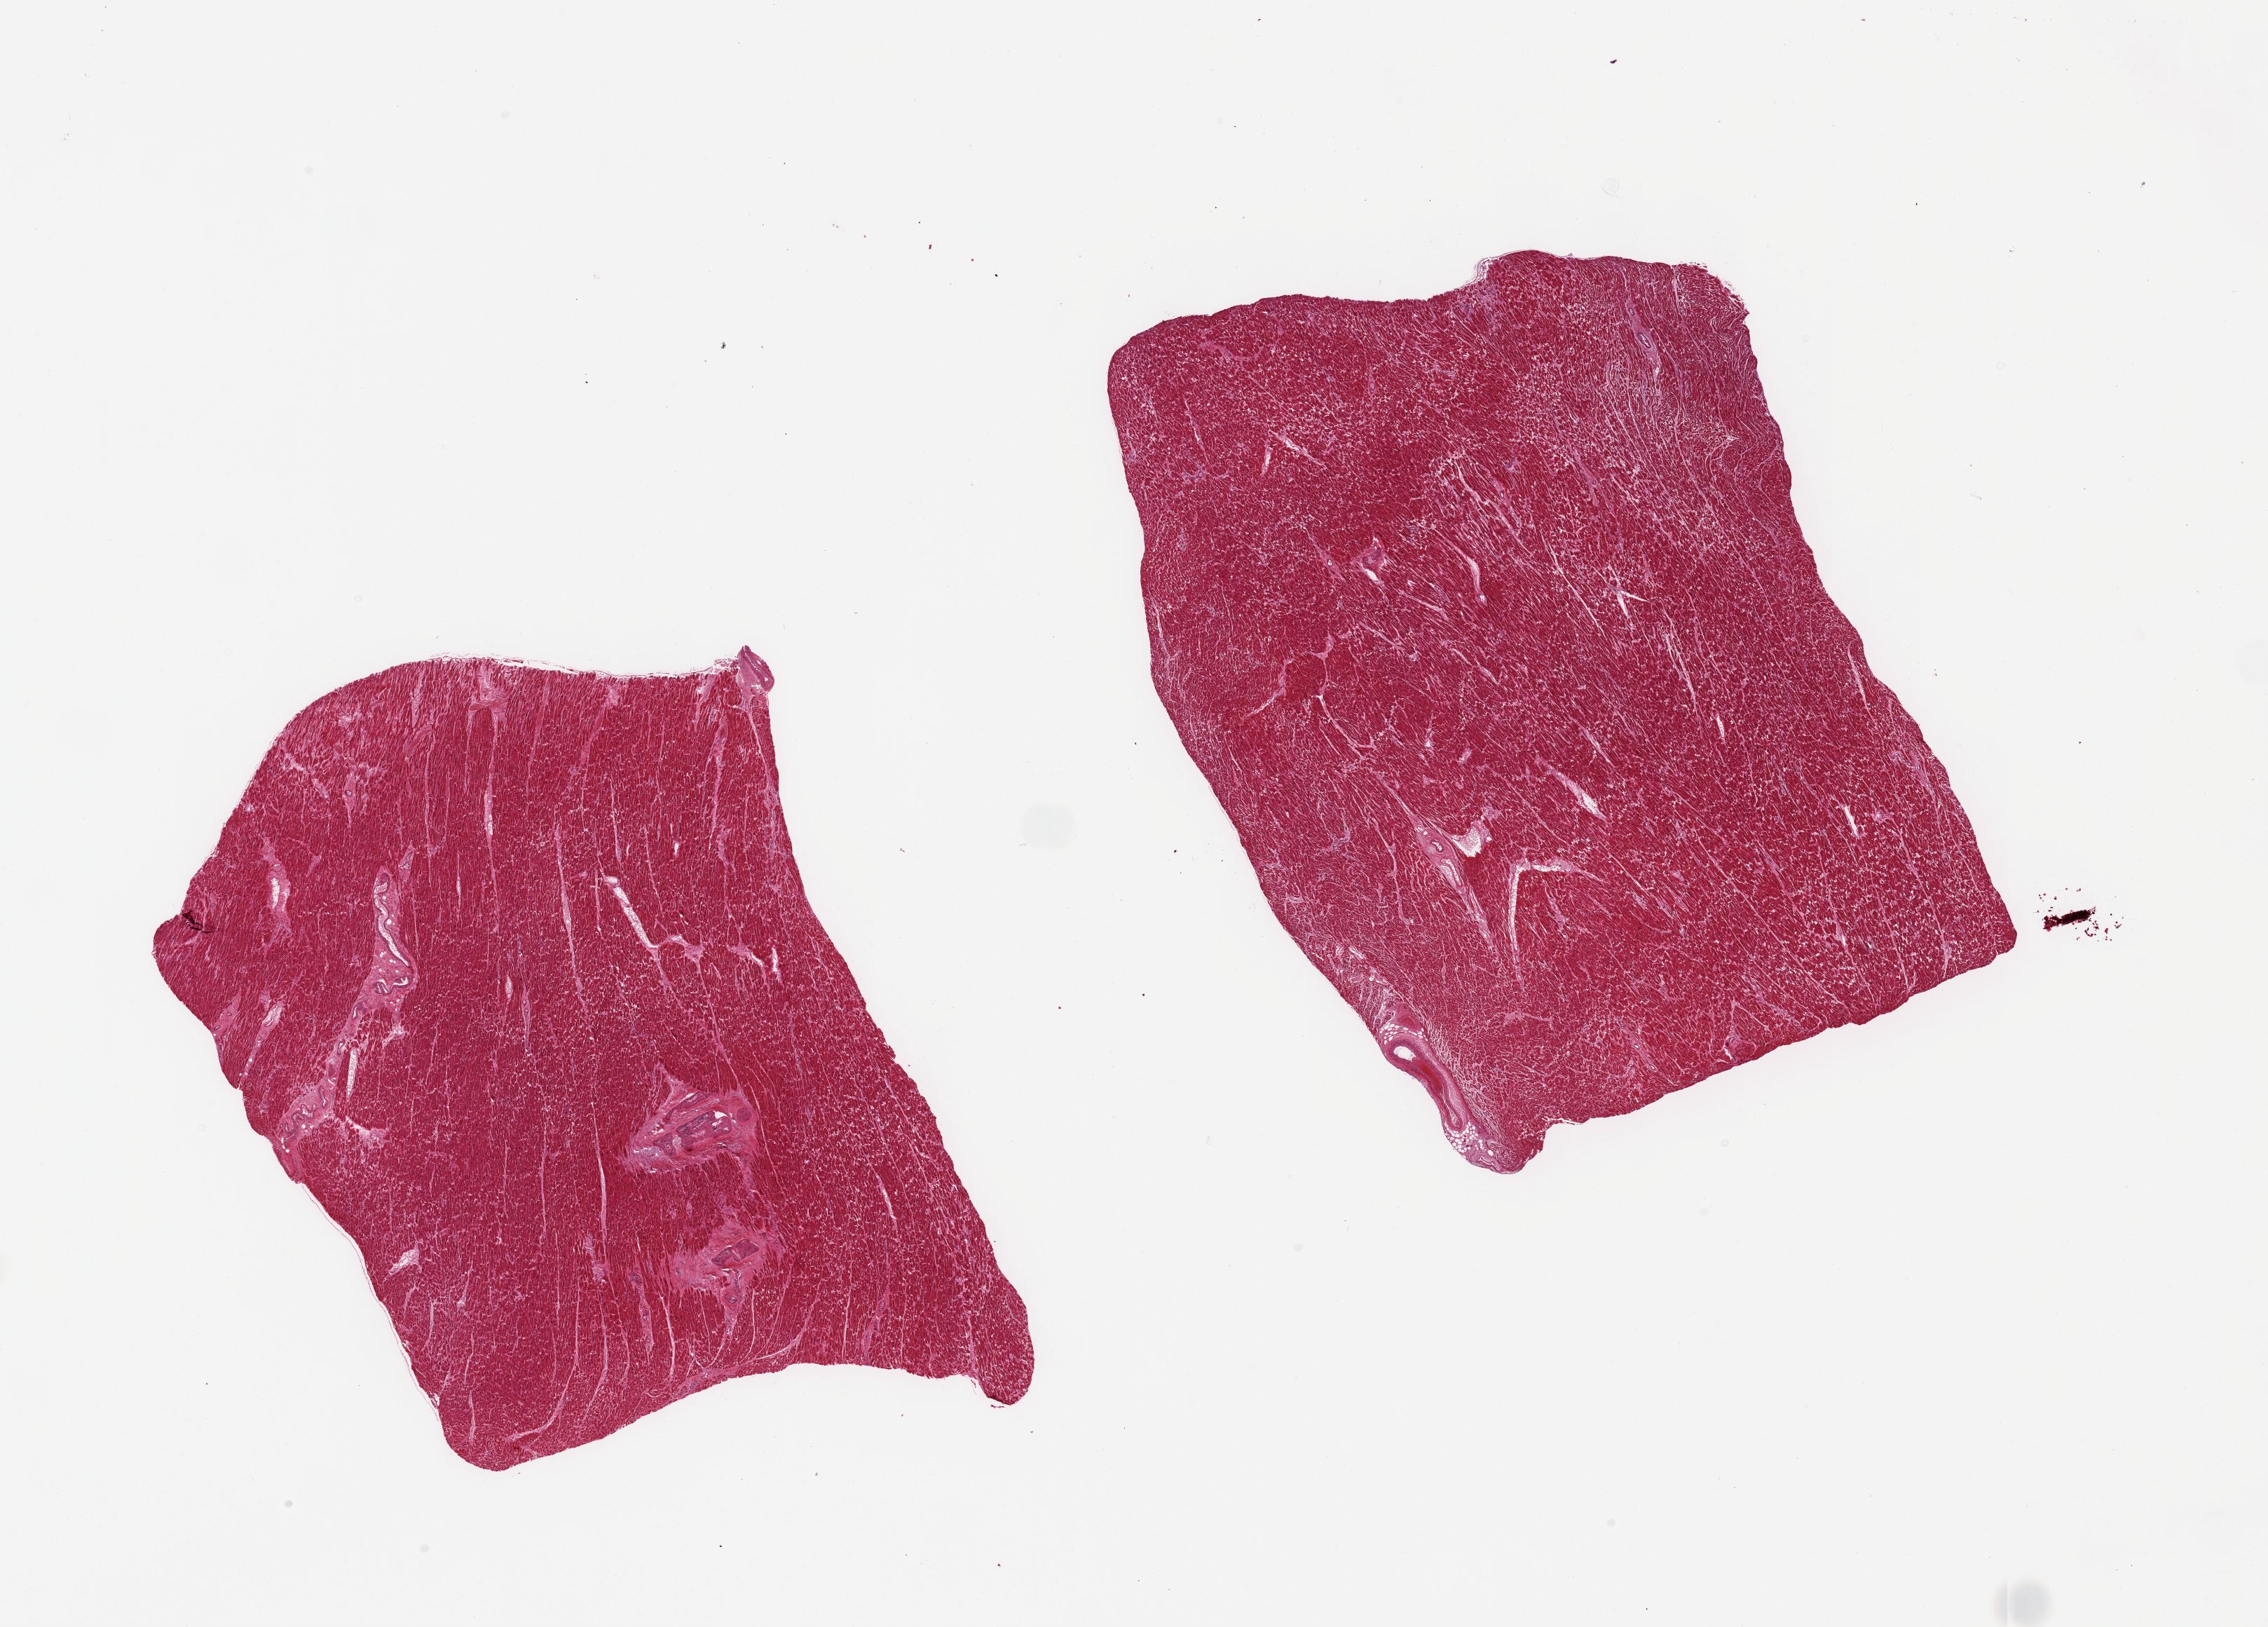
Whole-slide image, hematoxylin and eosin (H&E) stain, brightfield, shown as a low-resolution overview of the whole scanned area (about 25.6 x 18.4 mm); PAXgene-fixed paraffin-embedded (PFPE) section; sampled site (target tissue): heart; donor tissue sample. Donor sex: female.
Review note (as recorded): 2 pieces; moderate fiber fragmentation.